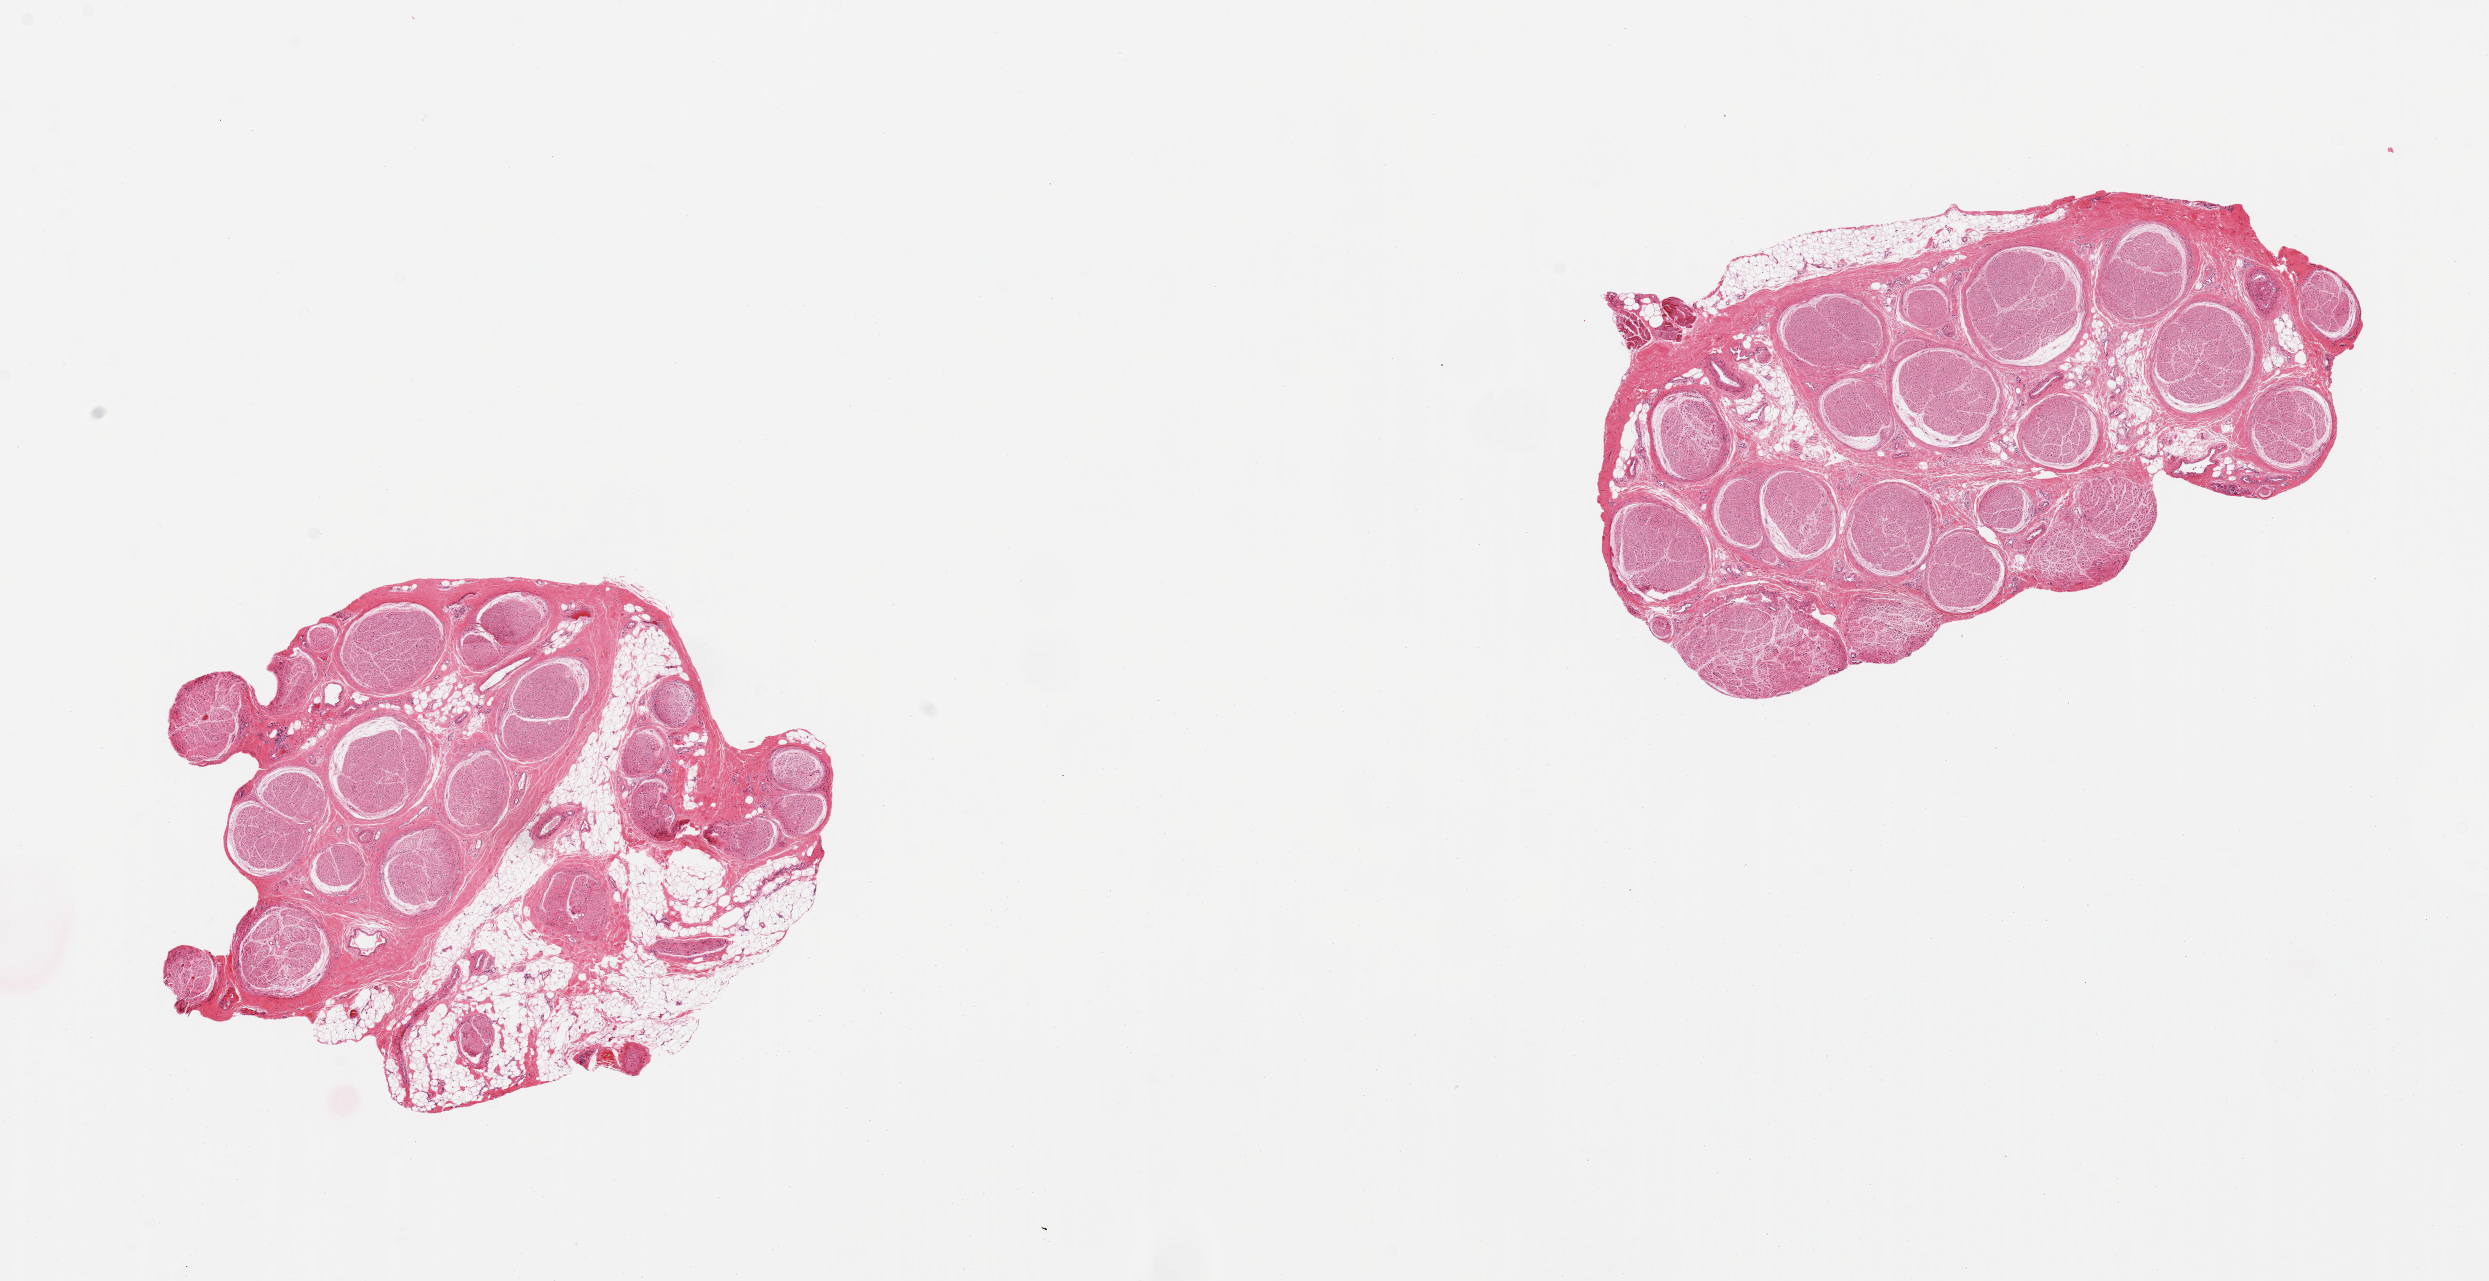
Digitized haematoxylin and eosin-stained section — low-resolution overview of the scanned area, about 19.7 x 10.1 mm (slide scanned at 20x). PAXgene-fixed paraffin-embedded (PFPE) section. Target tissue: tibial nerve. Tissue donor sample. Donor sex: male.
Pathologist's review note for this sample: 2 pieces; 1 has 40% internal & external fat; other has 10% internal & external fat.